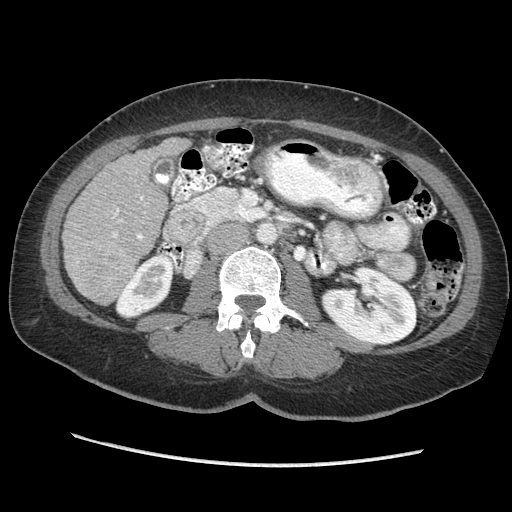
Contrast-enhanced abdominal CT (liver protocol), one axial slice. Slice 103 of 170 in the series (ordered by position). Reconstruction kernel STANDARD. 140 kVp. Soft-tissue window (W 400 / L 40 HU). 2.5 mm slice thickness. 512 × 512 image matrix. From the clinical record (not read from this slice): diagnosis: hepatocellular carcinoma (patient treated with transarterial chemoembolisation; whether this scan precedes or follows treatment is not stated here); TNM stage (as recorded): Stage-II; Child-Pugh class: A; tumour differentiation: no biopsy; tumour nodularity: multinodular.
Outlined on this slice (semi-automatic segmentation, software-assisted and operator-edited):
- liver parenchyma outside the tumour (the mass and vessels are separate outlines, so this box may not span the whole liver): bounding box (x1, y1, x2, y2) in pixels: (62, 138, 190, 304)
- liver vessels: (112, 196, 143, 240)